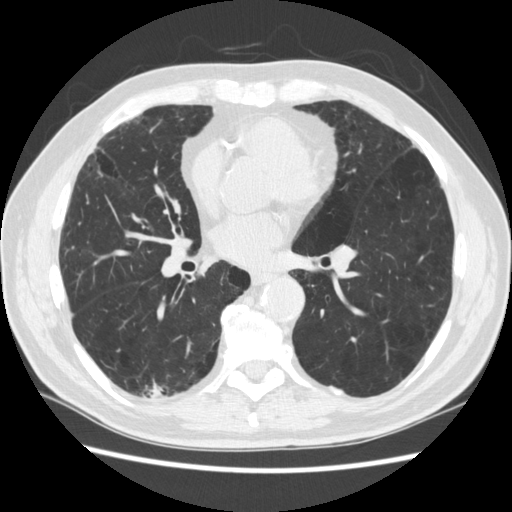
Low-dose screening chest CT, one axial slice. Position 129 of 266 along the scan axis. Reconstruction kernel STANDARD. Lung window (W 1500 / L -600 HU). 512 × 512 image matrix, field of view 360 × 360 mm.
Structures marked on this image (expert manual segmentation):
- lesion 1 (tumor, upper lobe of right lung): box from (x=152, y=387) to (x=160, y=397) px